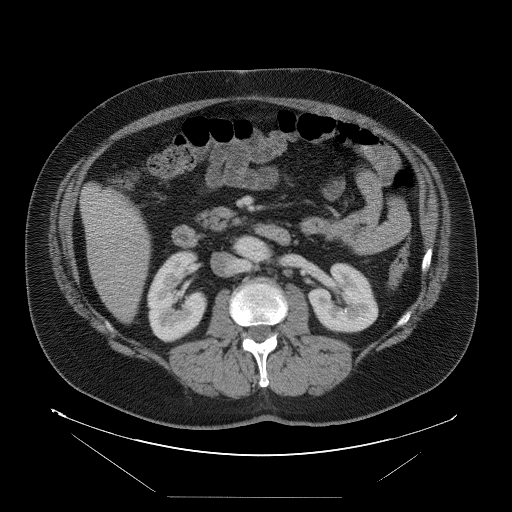
Contrast-enhanced abdominal CT, one axial slice; position 30 of 114 along the scan axis; intravenous contrast given; soft-tissue window (W 400 / L 40 HU); 512 × 512 image matrix. Male patient, age 61 years. From the clinical record (not read from this slice): diagnosis: colorectal cancer liver metastases, imaged before liver resection; multiple liver metastases: no; largest metastasis: 6.5 cm; chemotherapy before resection: no.
Structures marked on this image (manually delineated by an expert):
- liver: bounding box (x1, y1, x2, y2) in pixels: (82, 185, 152, 321)